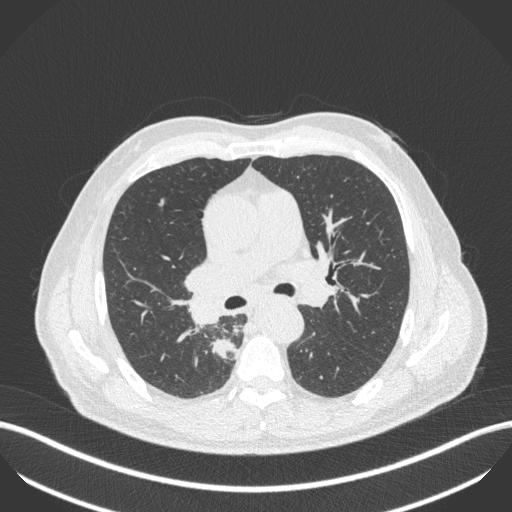
Chest CT, one axial slice. 100 kVp. Lung window (W 1500 / L -600 HU). 1 mm slice thickness. 512 × 512 image matrix. Patient: male, 61 years. Case-level facts recorded for this patient, not image findings: clinical TNM (as recorded): T1 N0 M0; histopathological grade: G3.
Annotated regions visible in this slice (bounding box drawn by a radiologist):
- lung tumour (recorded histology: small cell carcinoma): bounding box [x1, y1, x2, y2] px = [203, 334, 236, 361]